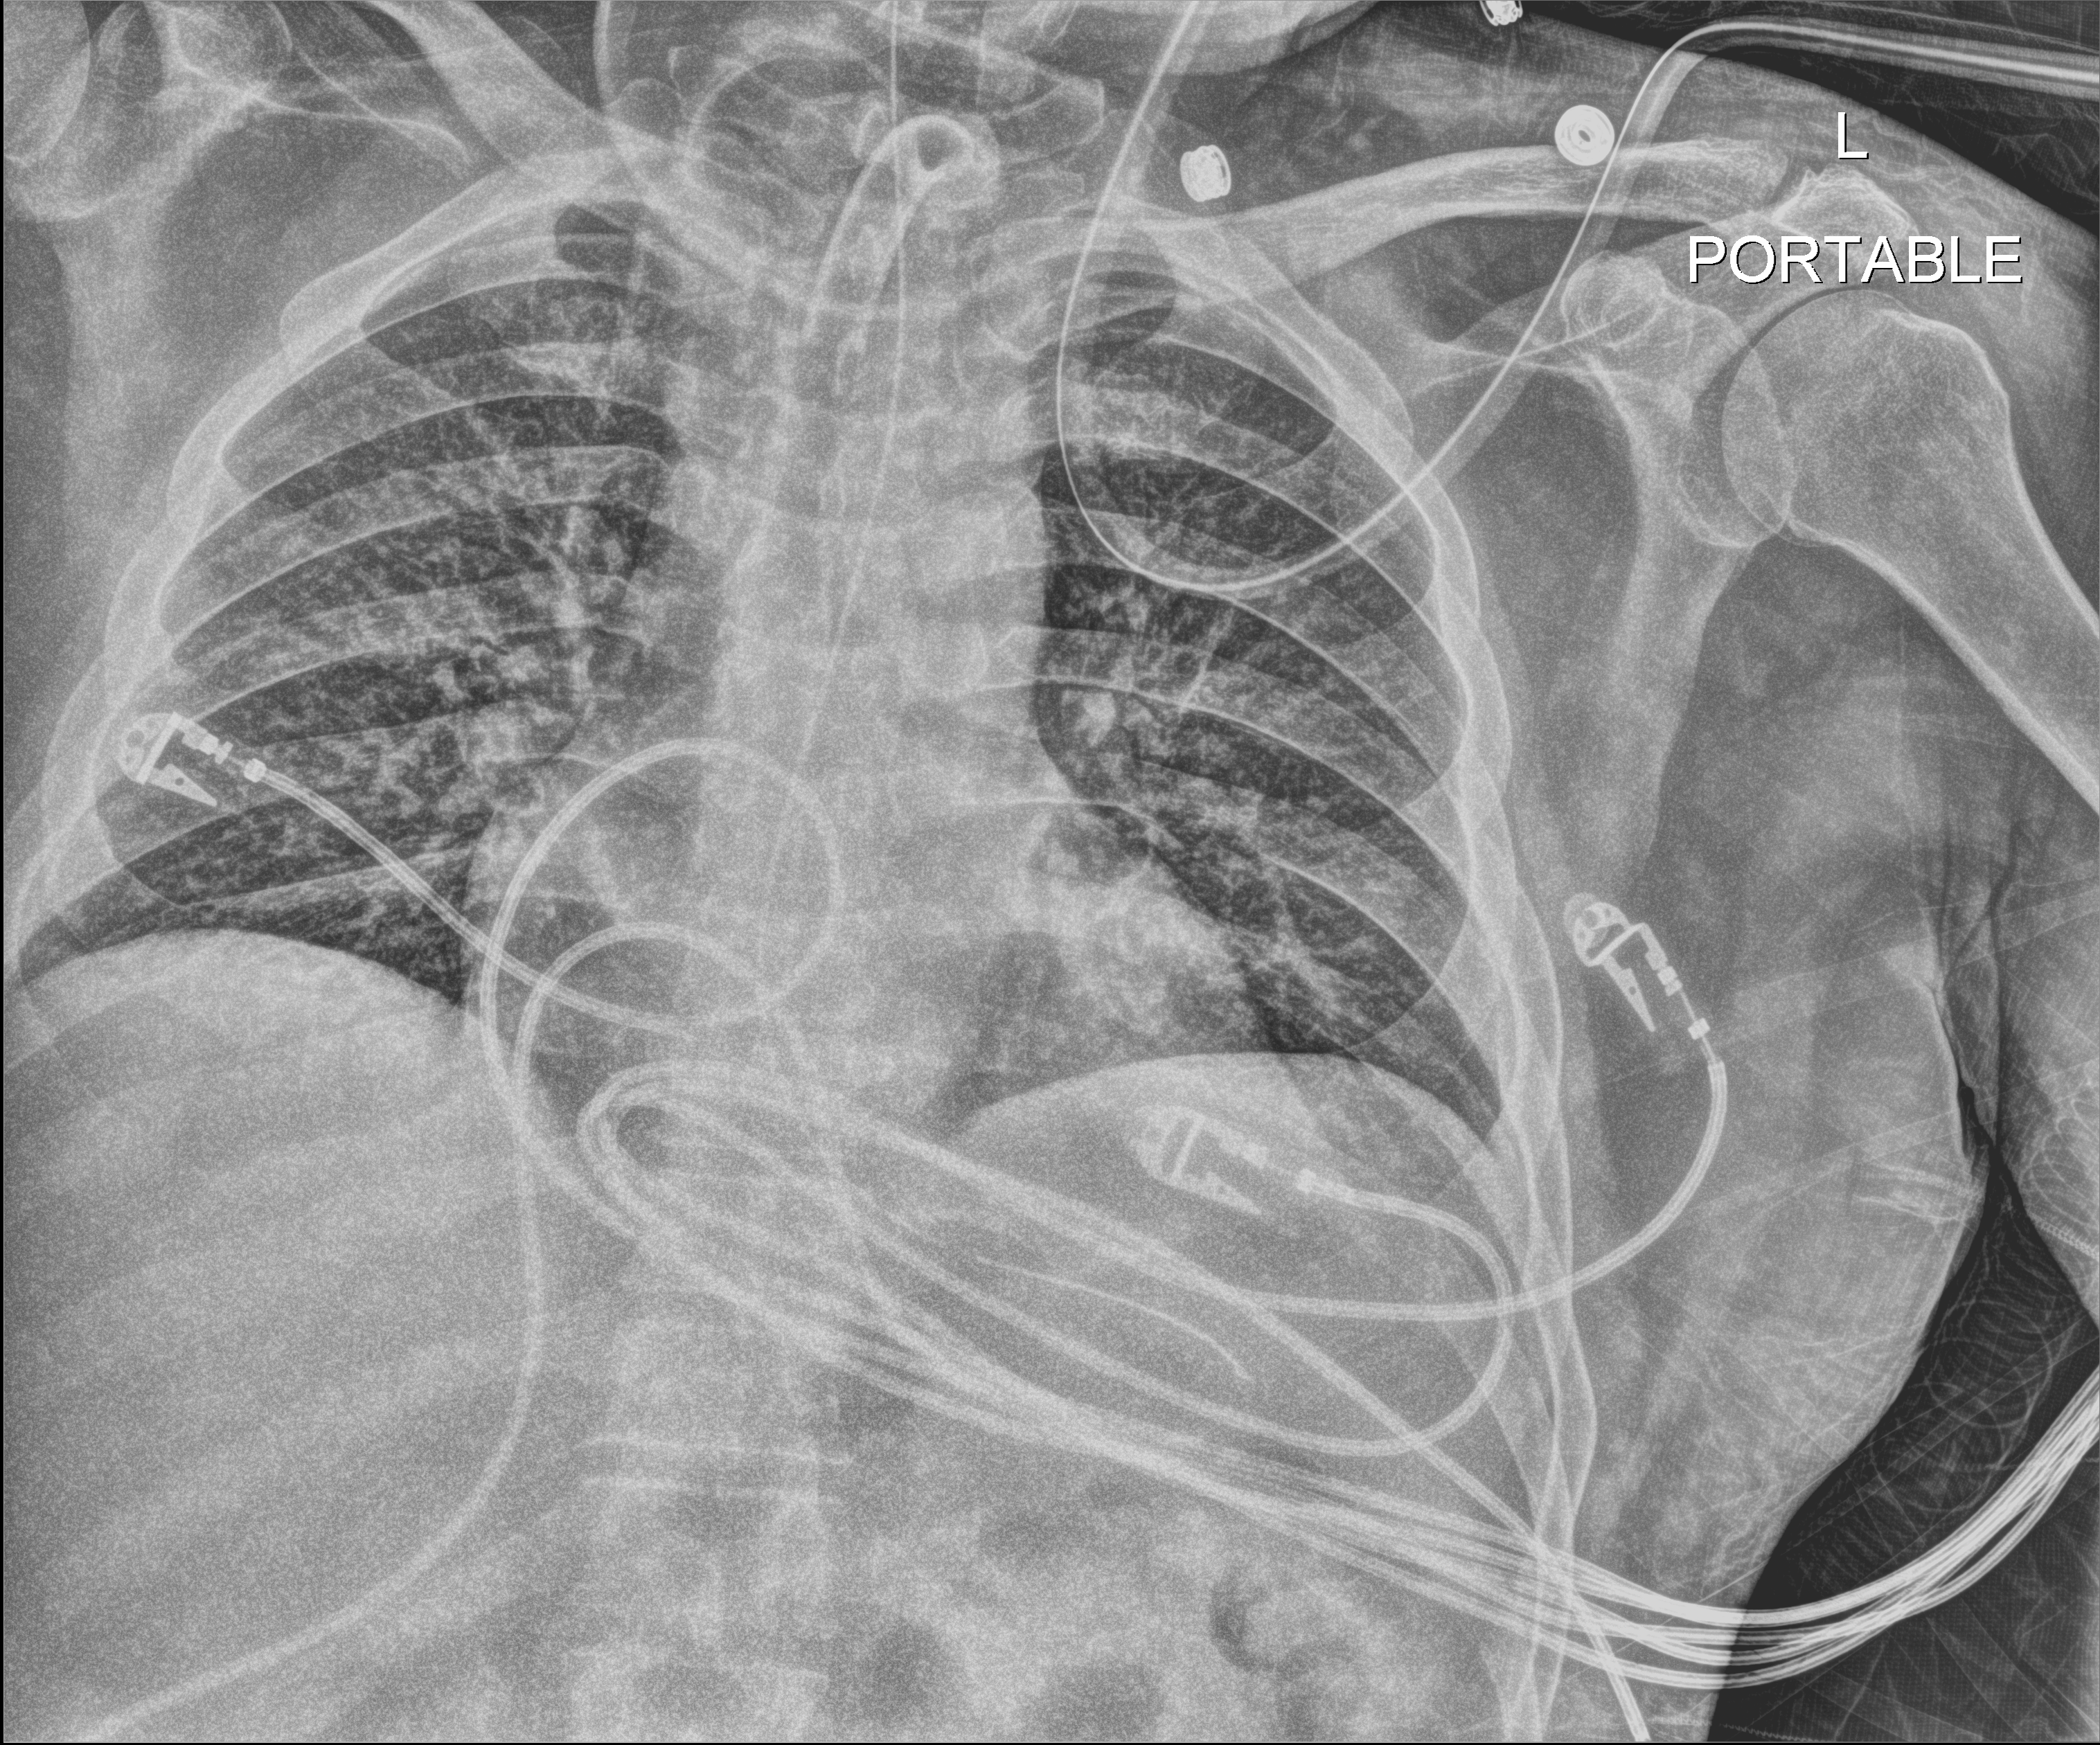
Bedside chest radiograph (digital radiography). Male patient hospitalised with COVID-19, age 18–59 years.
Admission-level facts for this patient (not findings on this image; timing relative to this image not recorded):
- admitted to intensive care during this hospital stay: yes
- mechanically ventilated during this hospital stay: yes